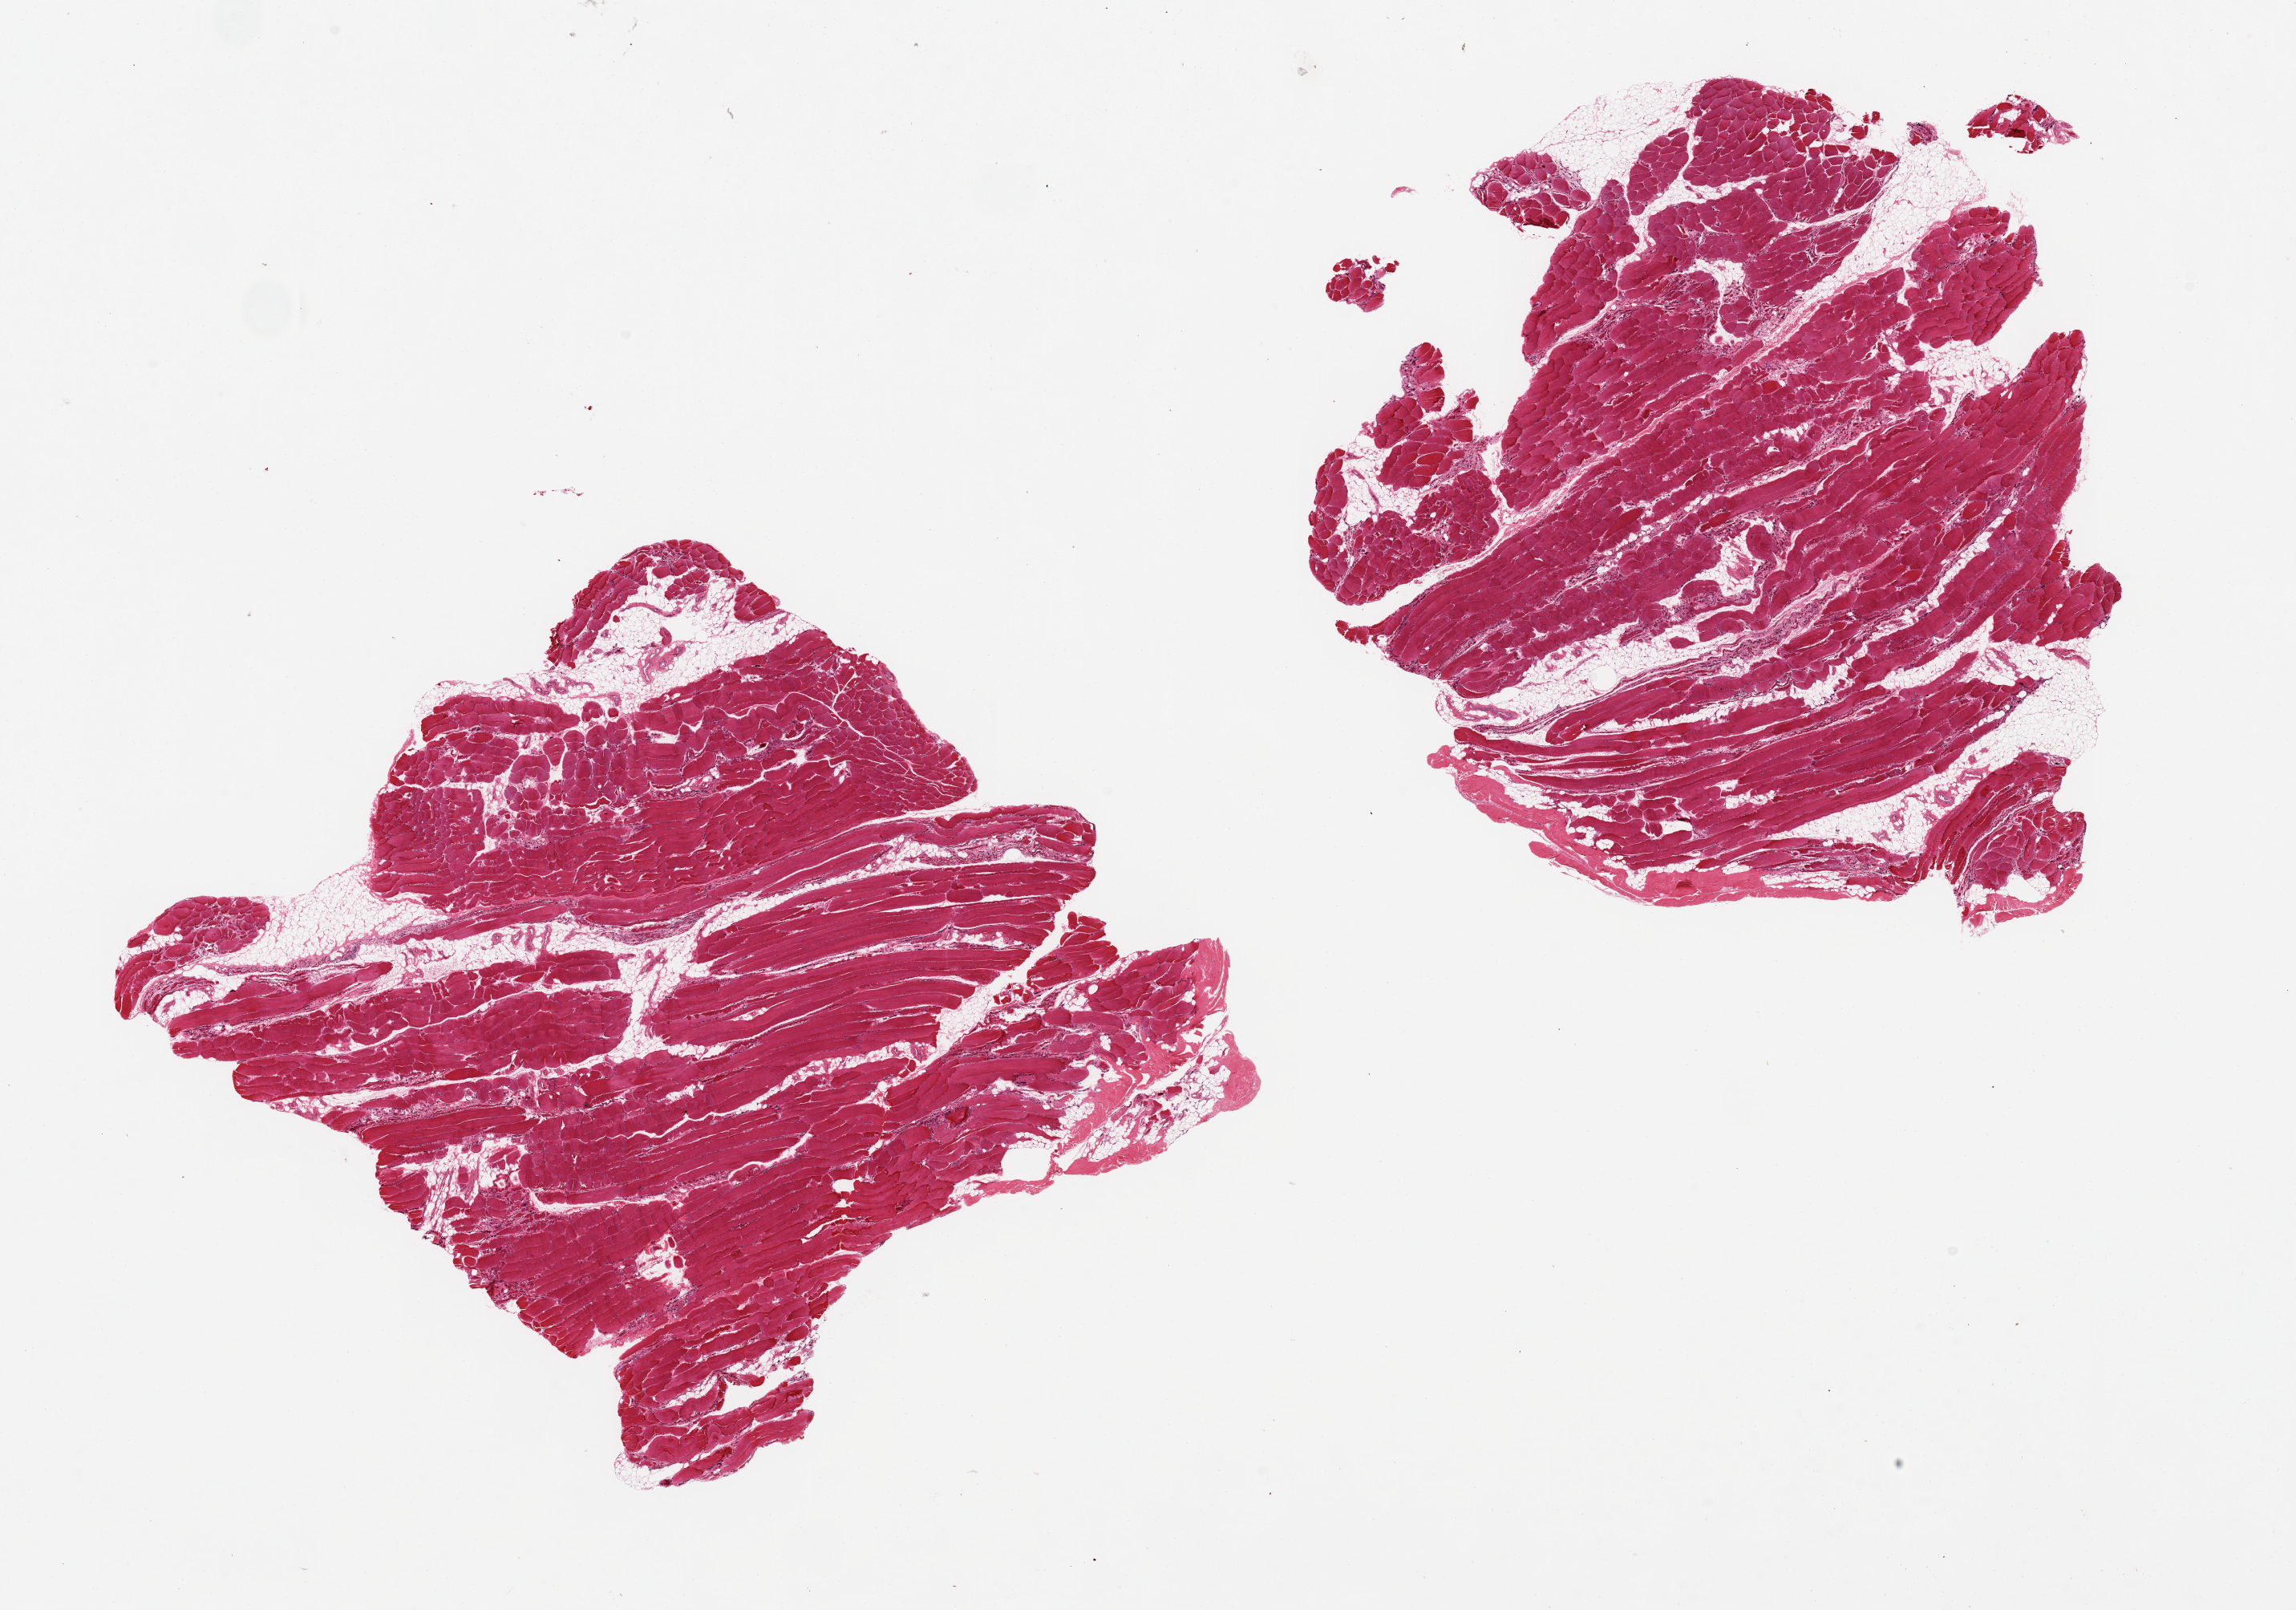
Hematoxylin and eosin (H&E) whole-slide image, a low-resolution overview of the entire scanned area, about 22.6 x 15.9 mm; PAXgene-fixed paraffin-embedded (PFPE) section; sampled site (target tissue): skeletal muscle; donor tissue sample. Donor sex: female.
Reviewer comment on this tissue sample: 2 pieces, 7x7 & 7x7 mm; ~10% adipose within pieces.